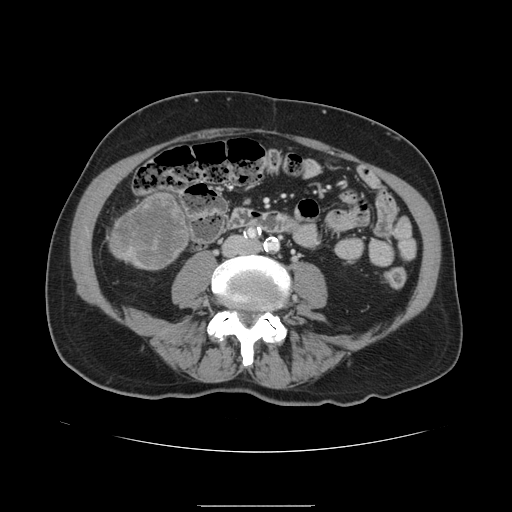
Contrast-enhanced abdominal CT, one axial slice. Slice 17 of 168 in the series (ordered by position). 120 kVp. Intravenous contrast given. Soft-tissue window (W 400 / L 40 HU). 2.5 mm slice thickness. 512 × 512 image matrix. Male patient, age 74 years. Case-level facts recorded for this patient, not image findings: diagnosis: colorectal cancer liver metastases, imaged before liver resection; multiple liver metastases: no; largest metastasis: 14.5 cm; disease in both lobes: yes.
Structures marked on this image (outlined manually by an expert reader):
- liver: bounding box (x1, y1, x2, y2) in pixels: (110, 189, 191, 271)
- liver metastasis: (113, 194, 188, 269)